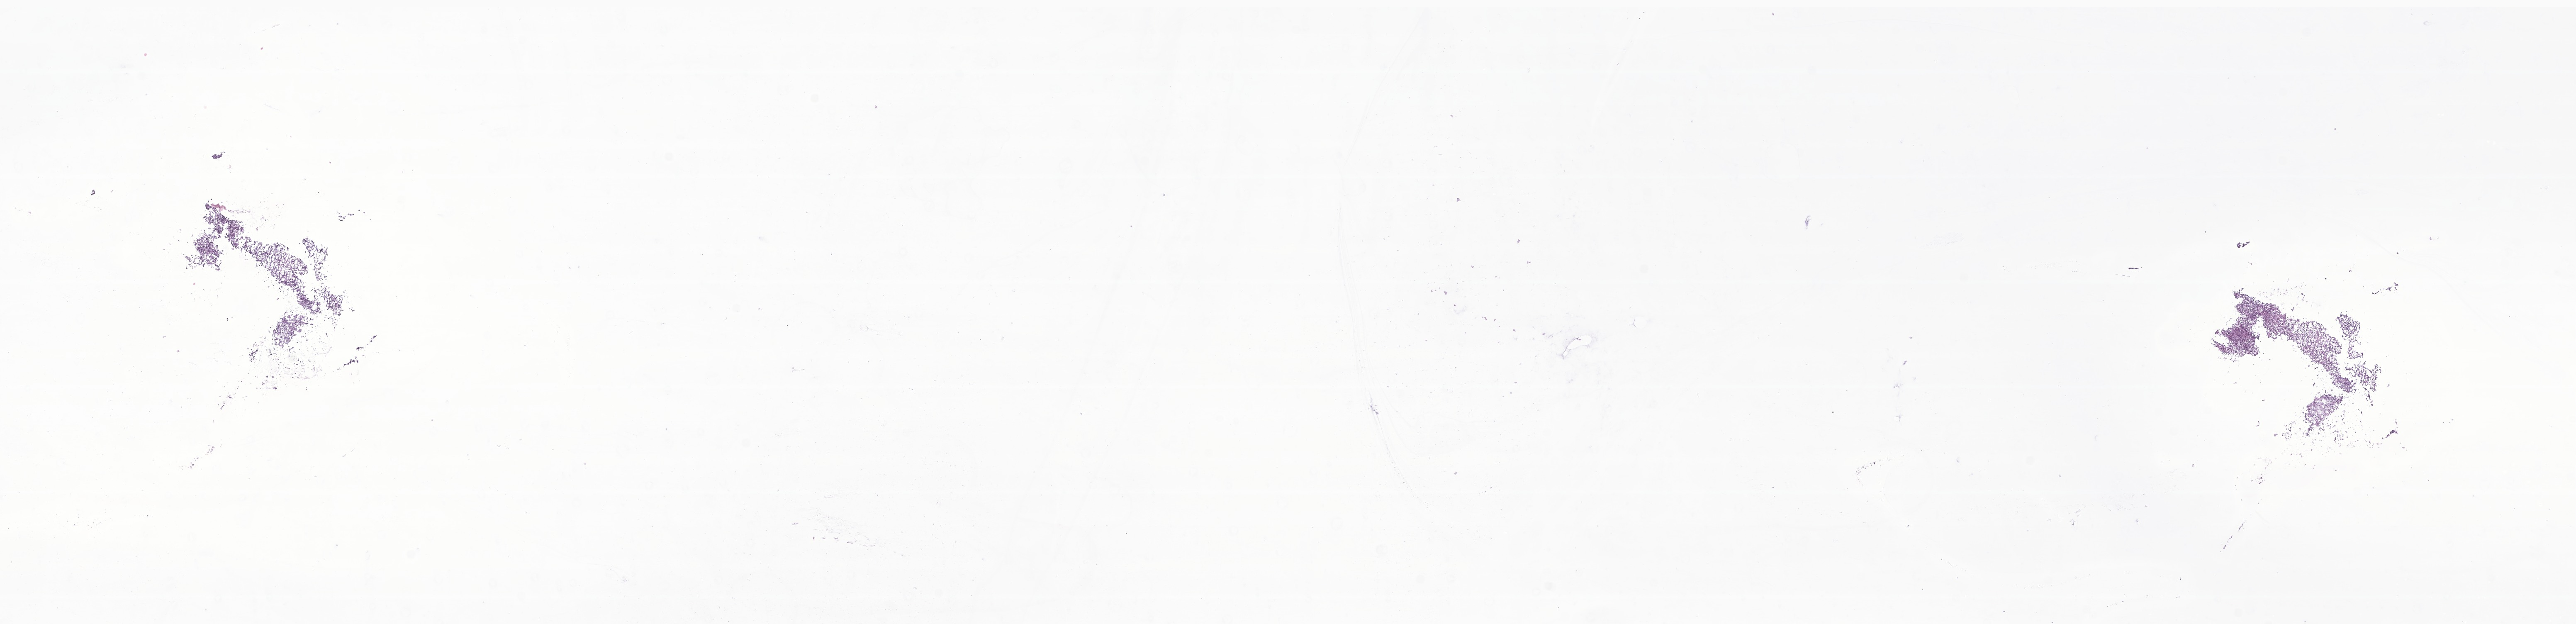
Whole-slide image, H&E stain of tumor tissue from the spinal cord — a low-resolution overview of the entire scanned area, about 26.2 x 6.3 mm; frozen section. Patient female; age 144 months.
Recorded diagnosis: Glioma, malignant.